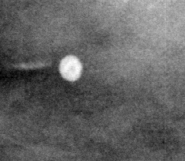
Crop from a digitized film mammogram around one marked abnormality, right breast, MLO view.
- Calcifications, morphology round and regular / lucent center / punctate, distribution diffusely scattered; BI-RADS assessment category 2; subtlety rating 5 on a 1 (subtle) to 5 (obvious) scale; benign; no additional work-up was recommended (benign without callback).